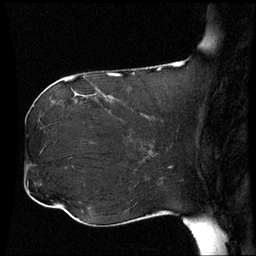
Breast MRI (dynamic contrast-enhanced), one sagittal slice. Slice 26 of 60 in the series (ordered by position). Dynamic contrast-enhanced series, image 2 of 3 at this slice position (ordered by acquisition). 1.5 T. TE 4.2 ms, TR 8.9 ms. 2.5 mm slice thickness. 256 × 256 image matrix, field of view 230 × 230 mm. Female patient, age 42 years. From the clinical record (not read from this slice): setting: breast cancer imaged before/during neoadjuvant chemotherapy; receptor status: HER2-positive.
Outlined on this slice (semi-automatically segmented with operator editing):
- analysis volume of interest (the breast-tissue region the enhancement analysis was run in; not a lesion): bounding box <106,102,173,150> (left, top, right, bottom; pixels)
- tumour enhancement mask (voxels above the 70 % enhancement threshold inside the analysis volume of interest): <140,113,148,118>